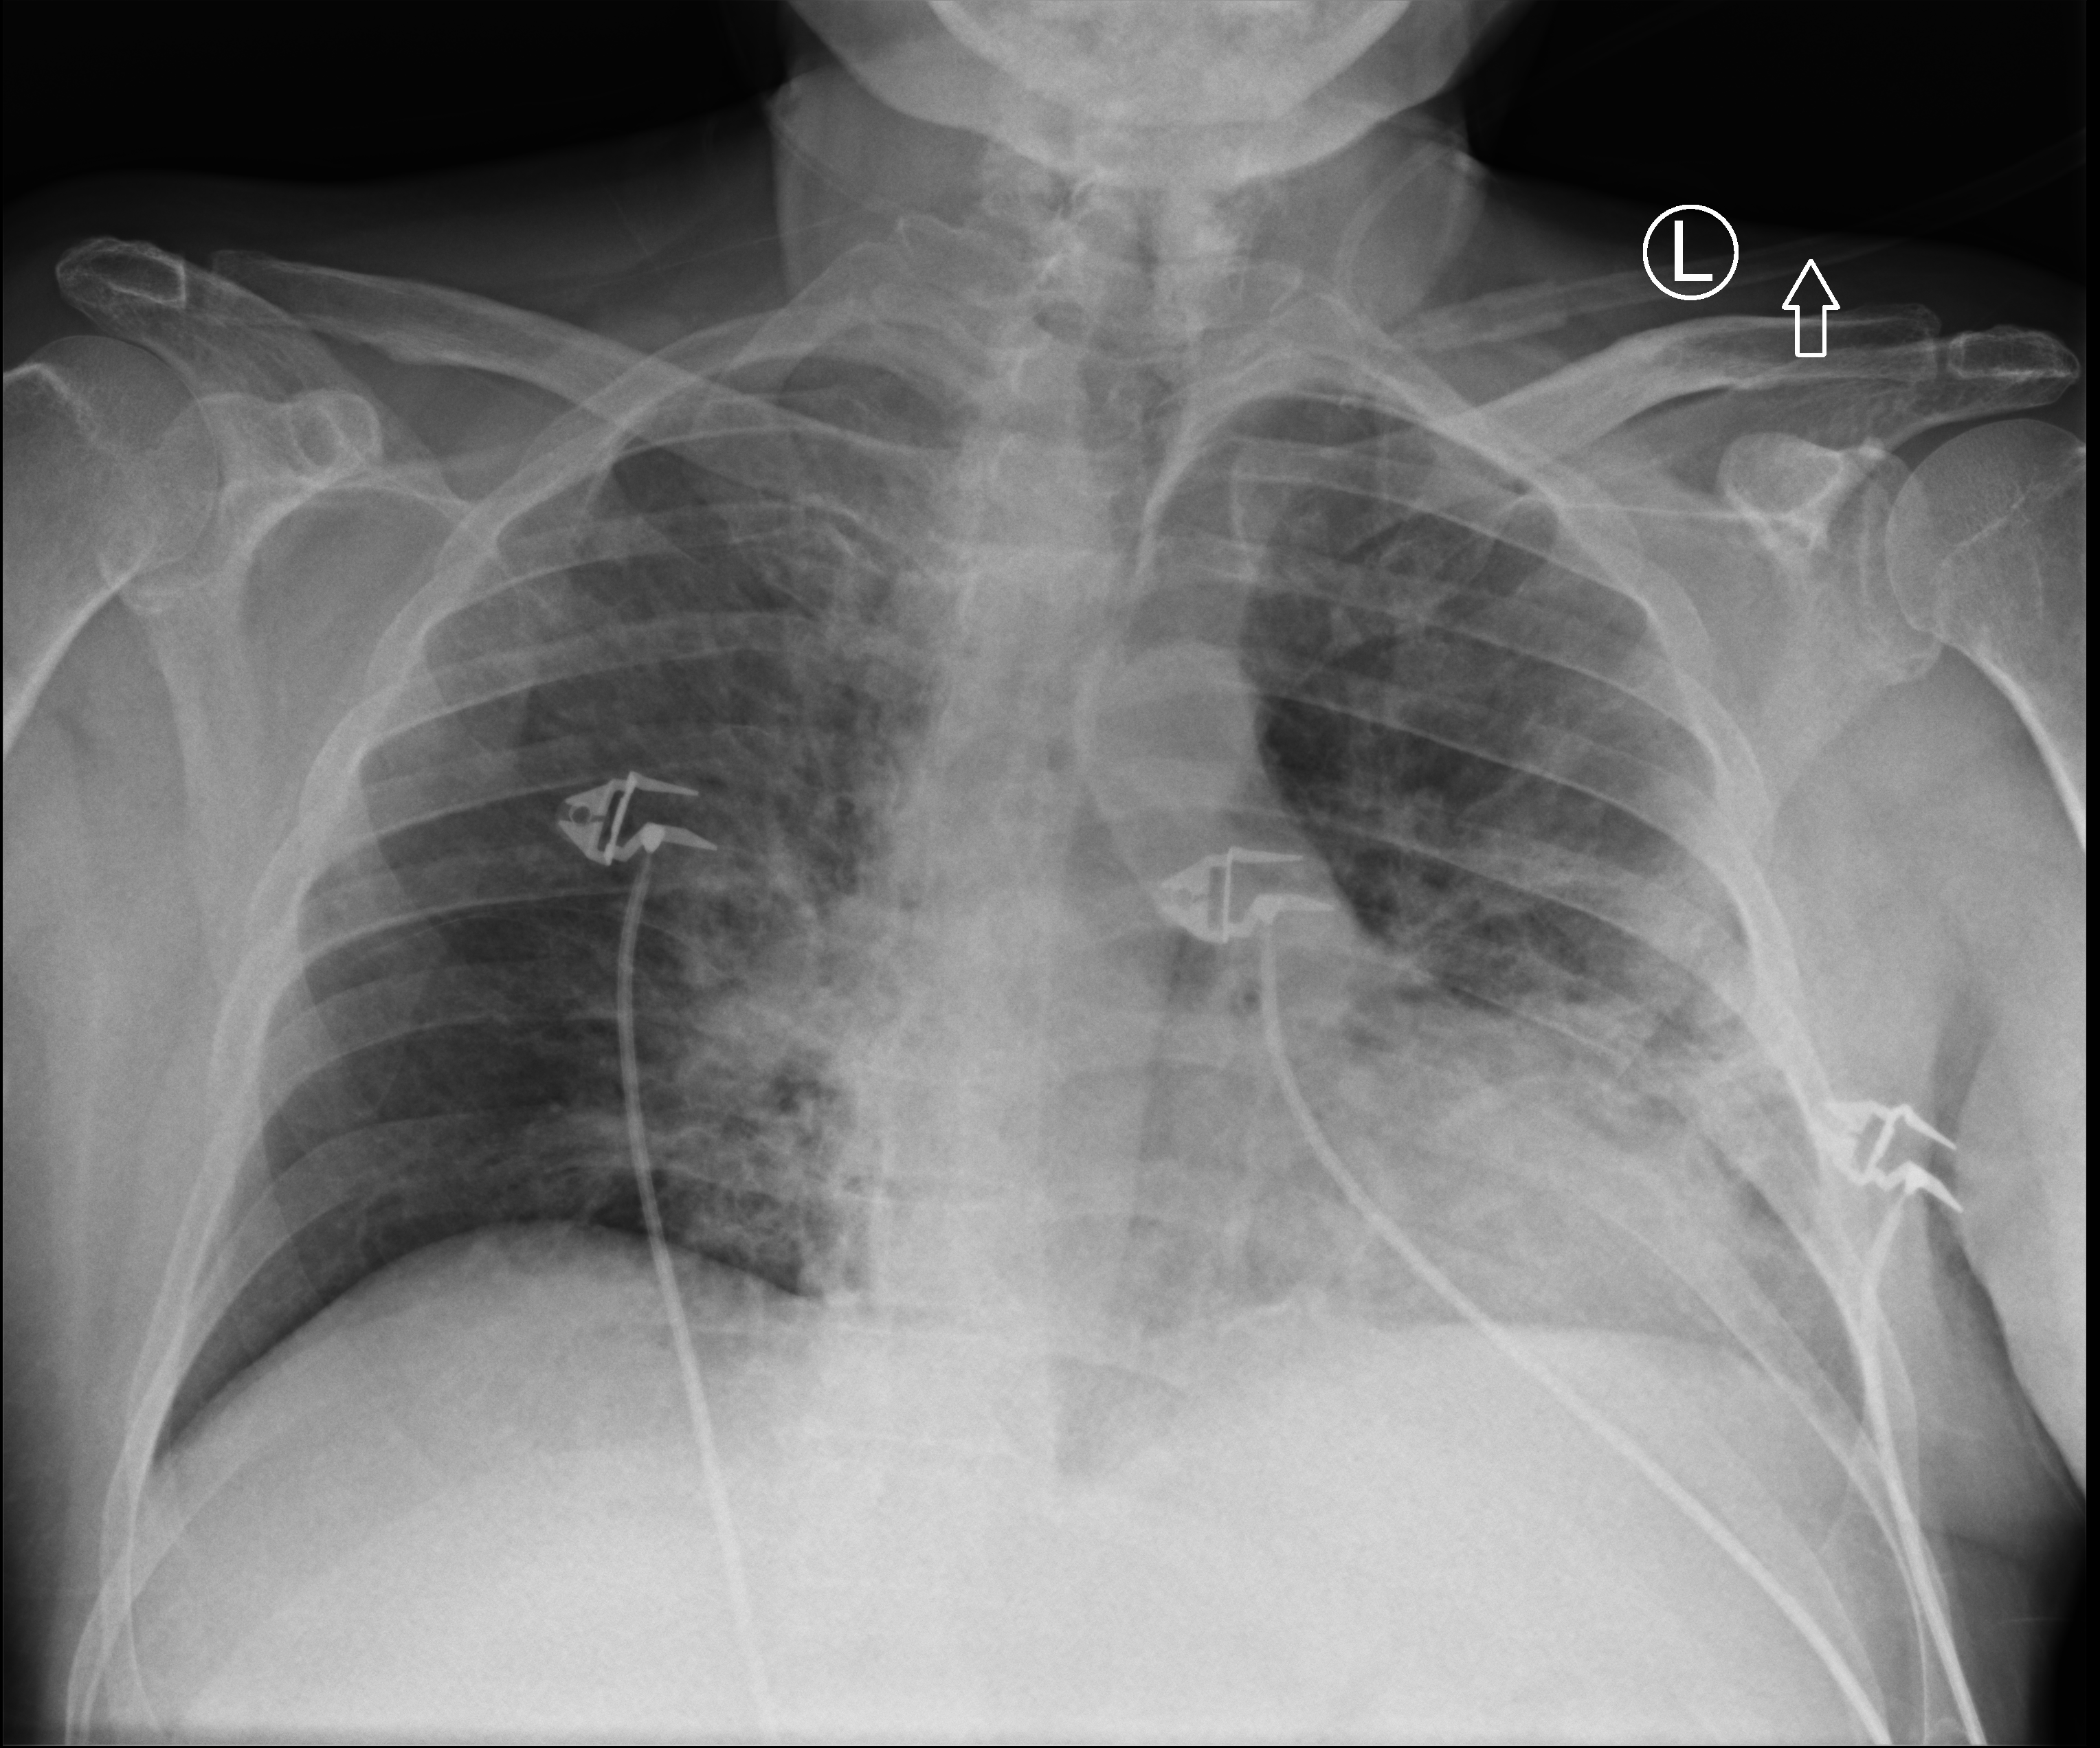
Portable chest radiograph; anteroposterior (AP) projection. Male patient hospitalised with COVID-19, age 60–74 years.
Hospital-stay facts (about this admission, not read from this image; timing relative to this image not recorded):
- COPD (admission record): no
- admitted to intensive care during this hospital stay: yes